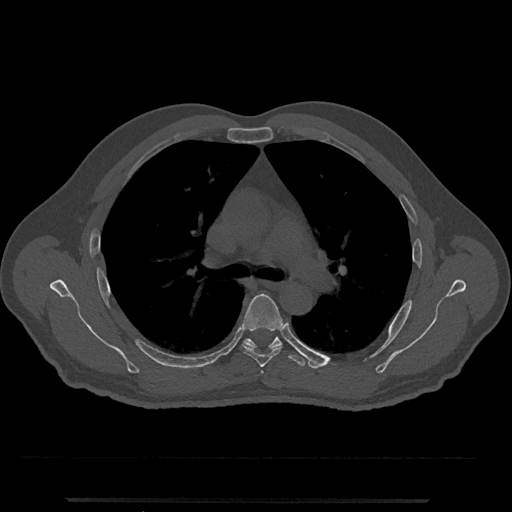
CT including the spine, one axial slice; slice 774 of 797 in the series (ordered by position); reconstruction kernel Br40s/3; 120 kVp; bone window (W 1800 / L 400 HU); 512 × 512 image matrix. Male patient, age 63 years. From the clinical record (not read from this slice): primary cancer: prostate.
Annotated regions visible in this slice (semi-automatically segmented with operator editing):
- T5 vertebra: bounding box [x1, y1, x2, y2] px = [239, 293, 284, 367]
- T6 vertebra: [243, 336, 306, 366]